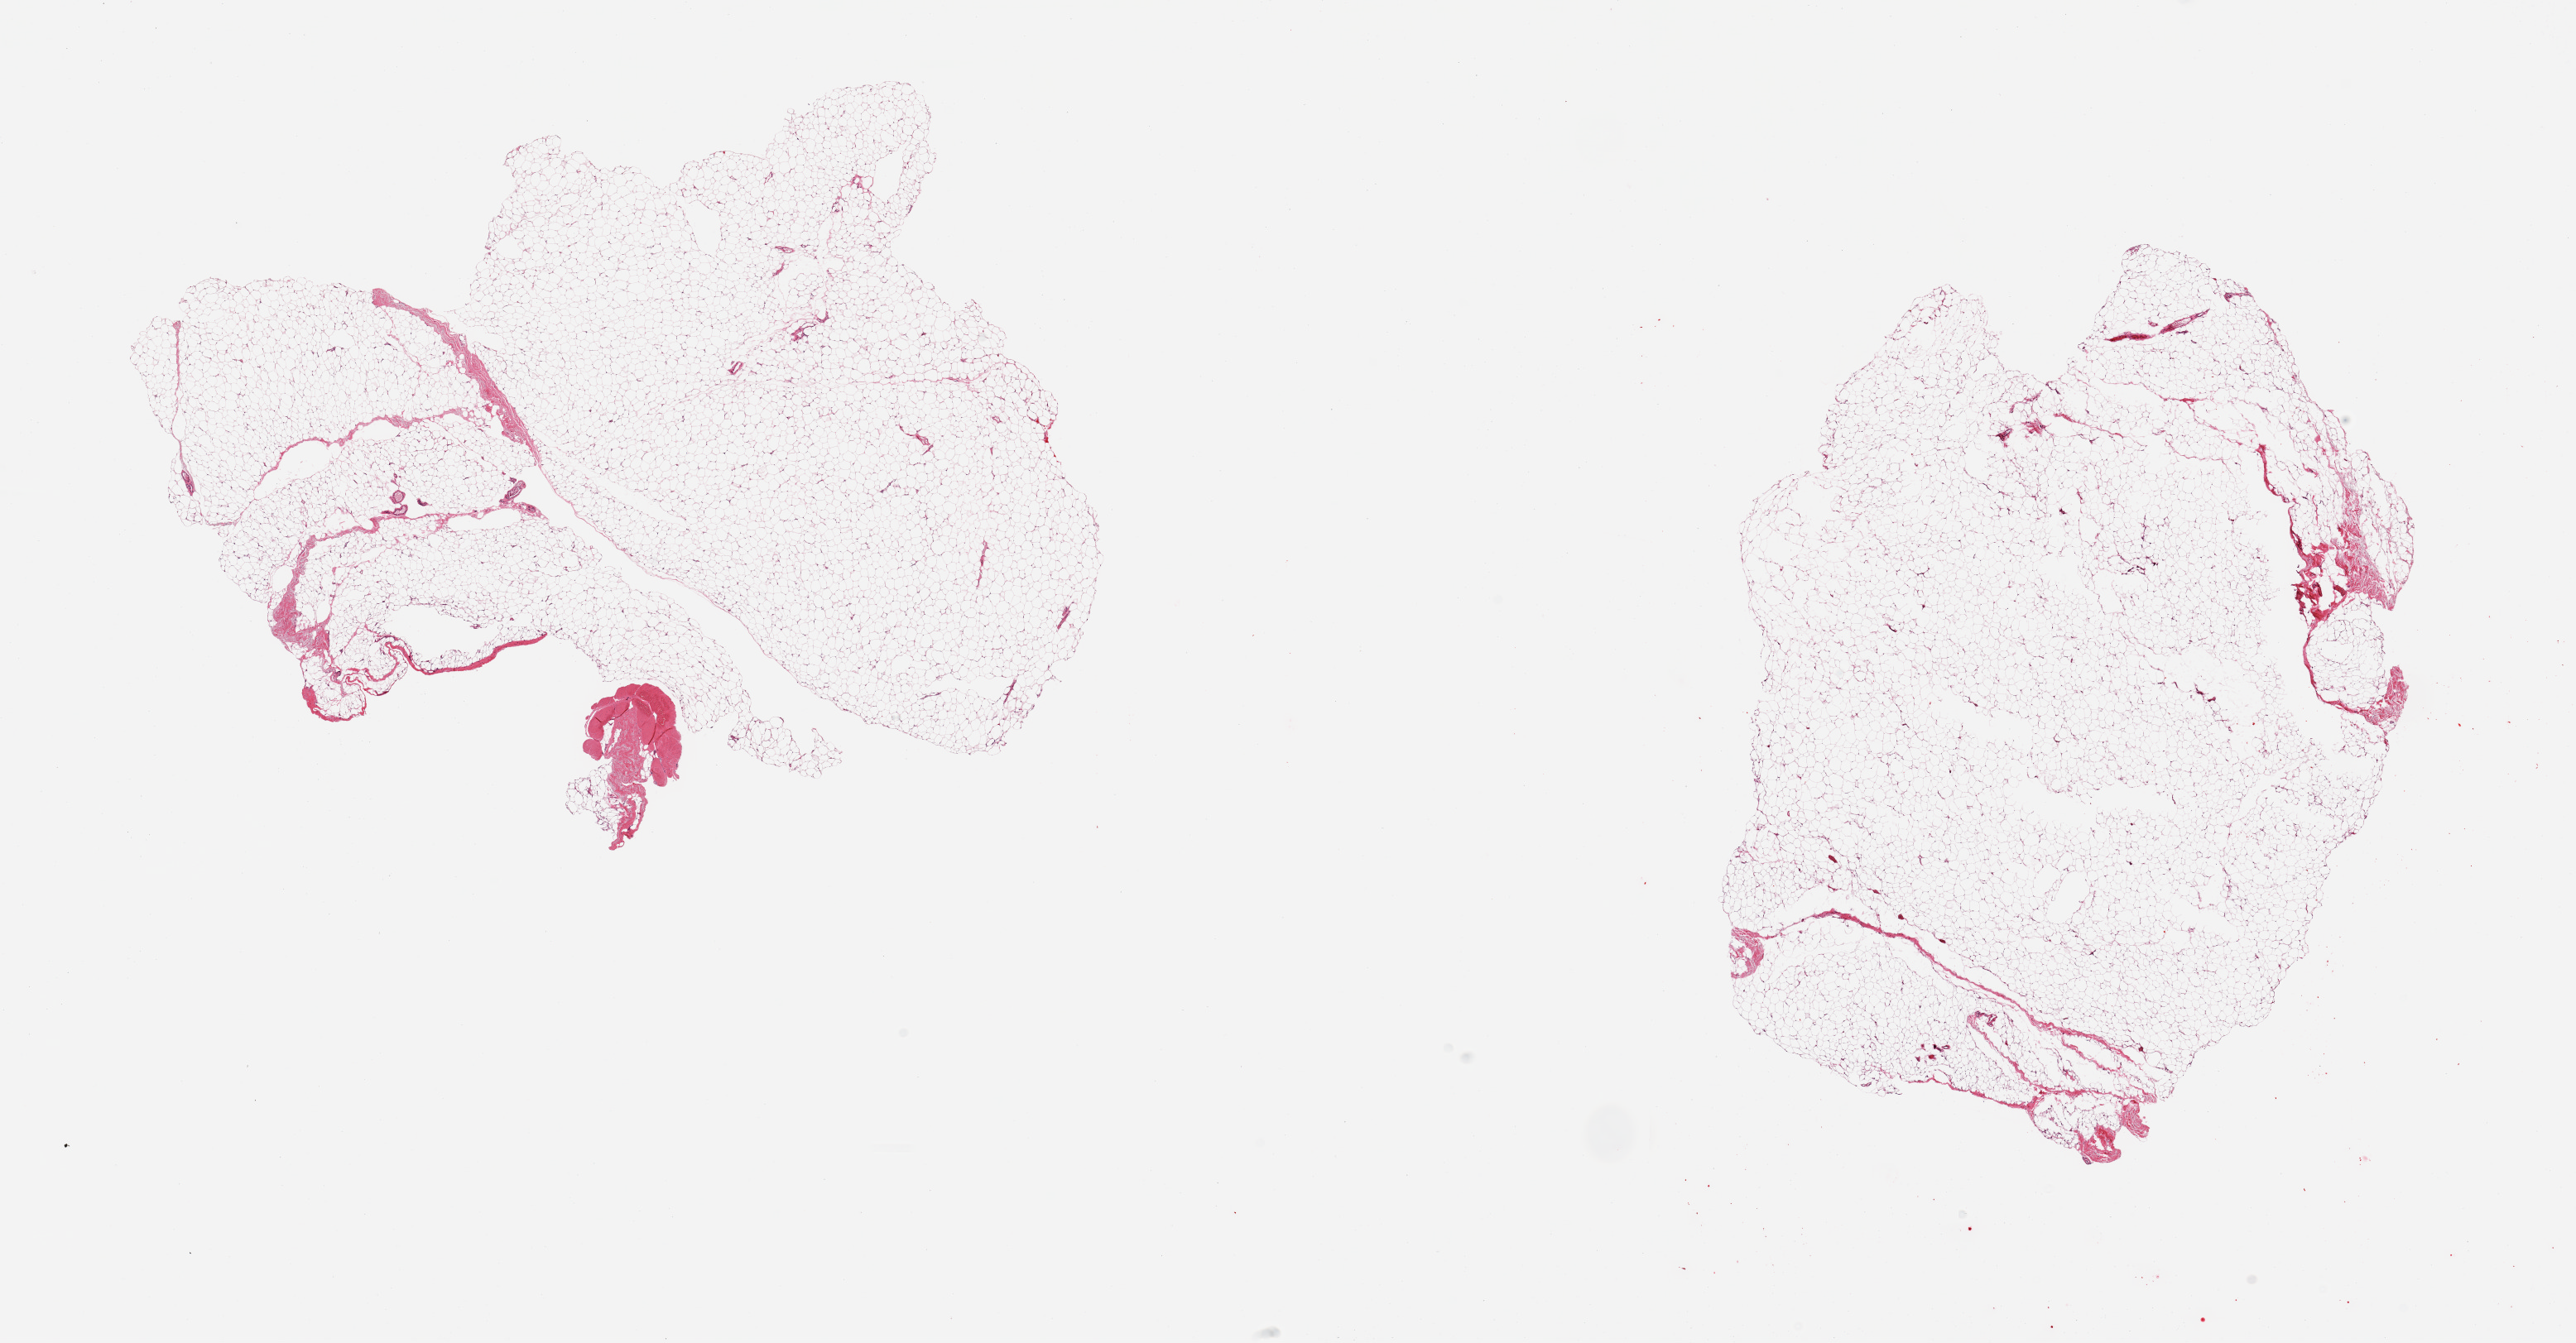
Whole-slide image, hematoxylin and eosin (H&E) stain, whole scanned area (about 24.6 x 12.8 mm) shown as a low-resolution overview, PAXgene-fixed paraffin-embedded (PFPE) section, target tissue: breast, donor tissue sample.
Pathologist's review note for this sample: 2 pieces; all fat no mammary tissue.